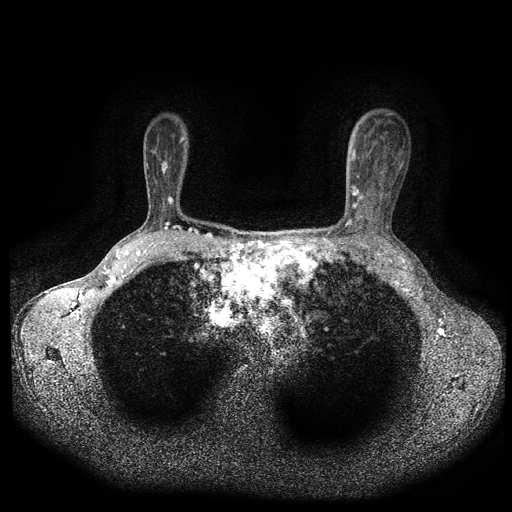
Breast MRI (dynamic contrast-enhanced, multi-phase), one axial slice; slice 72 of 116 in the series (ordered by position); dynamic contrast-enhanced series, time point 2 of 5 at this slice position (early post-contrast); 1.5 T; TE 2.7 ms, TR 5.4 ms; 2 mm slice thickness; 512 × 512 image matrix, field of view 330 × 330 mm. Female patient, age 49 years.
Outlined on this slice (semi-automatically segmented with operator editing):
- breast lesion (labelled benign in the annotation): bounding box <159,156,172,178> (left, top, right, bottom; pixels)